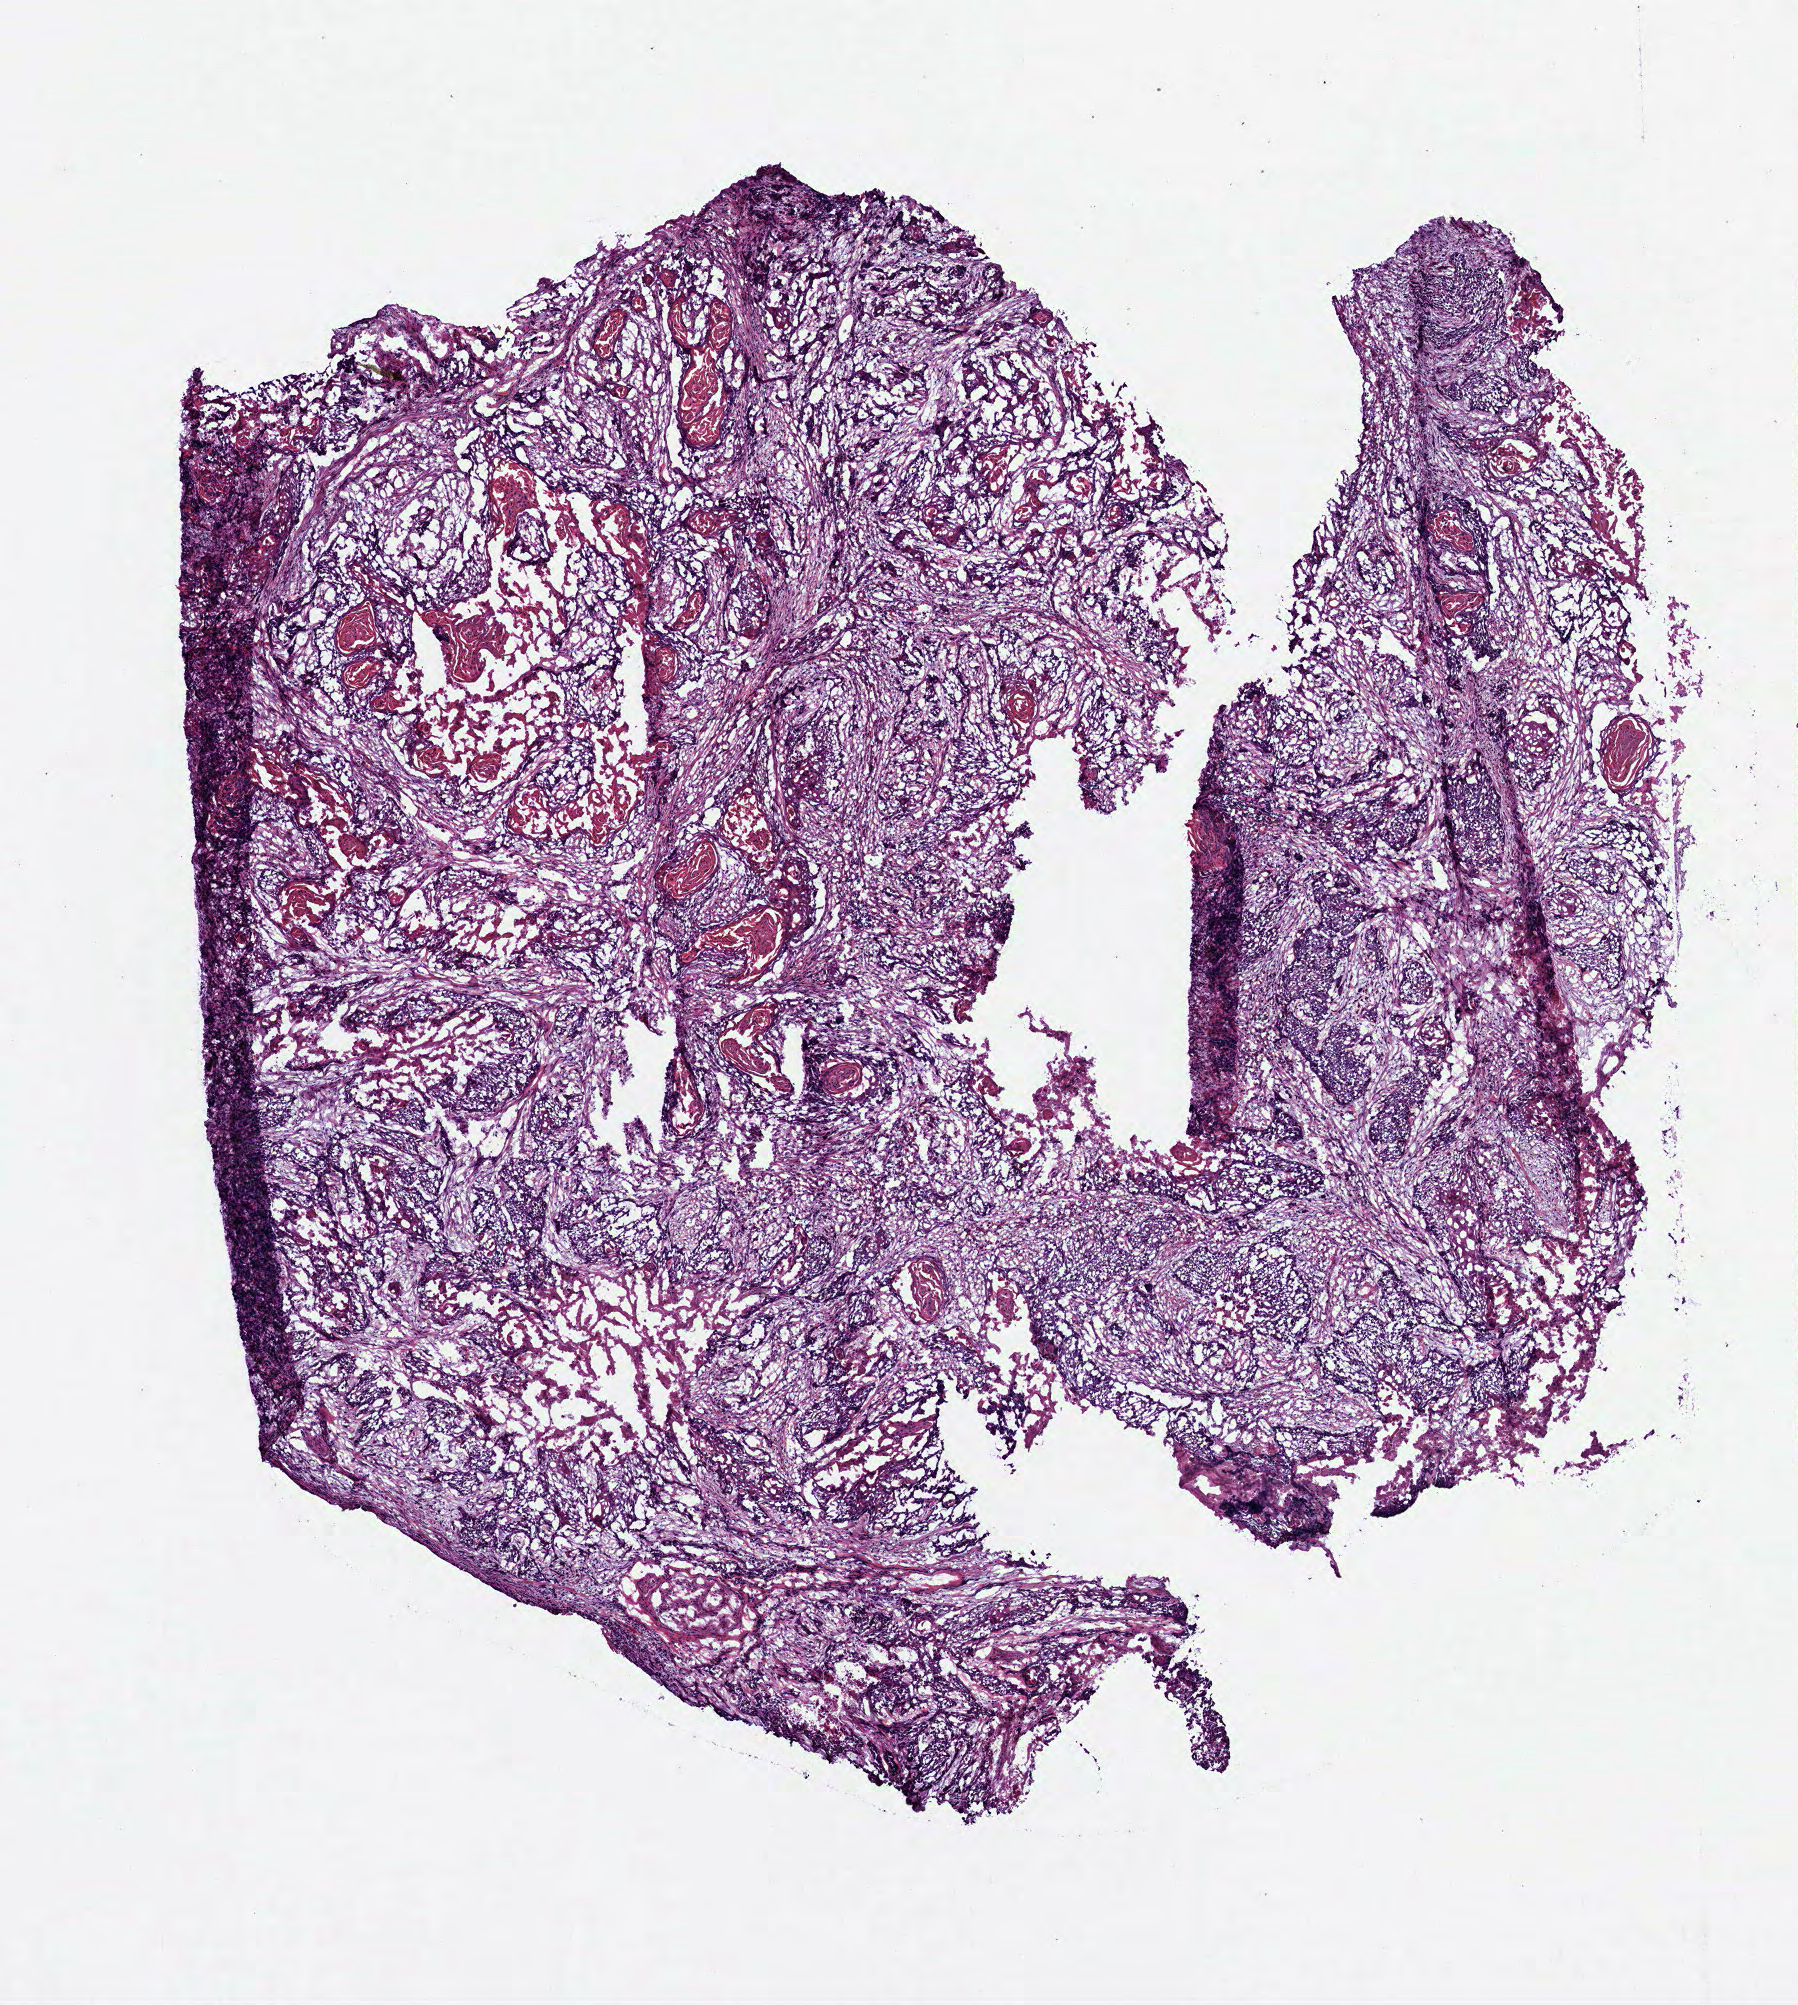
Whole-slide histology image, Hematoxylin and eosin (H&E) stained — whole scanned area (about 7.3 x 8.1 mm) shown as a low-resolution overview. Frozen section from the bottom of the tissue portion. Head and neck, primary tumour sample. Male, age 66 years at initial diagnosis. Histologic grade: G2 (moderately differentiated). Pathologist review of this section (percent, as recorded): tumour cells 75%, tumour nuclei 75%, normal cells 0%, stromal cells 20%, necrosis 5%.
* TNM: T4a N2c M0
* AJCC pathologic stage: IVA (6th edition)
* pathologic diagnosis: Squamous cell carcinoma, NOS (tongue, NOS)